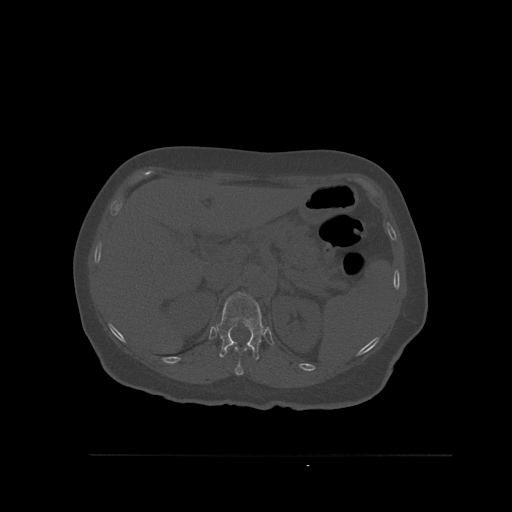
CT including the spine, one axial slice; slice 289 of 527 in the series (ordered by position); bone window (W 1800 / L 400 HU); 1.5 mm slice thickness; 512 × 512 image matrix. Patient: female, 73 years. From the clinical record (not read from this slice): primary cancer: breast; vertebrae with lytic lesions (as recorded): L2.
Outlined on this slice (semi-automatic segmentation, software-assisted and operator-edited):
- T11 vertebra: bounding box [x1, y1, x2, y2] px = [234, 346, 247, 376]
- T12 vertebra: [216, 292, 264, 360]